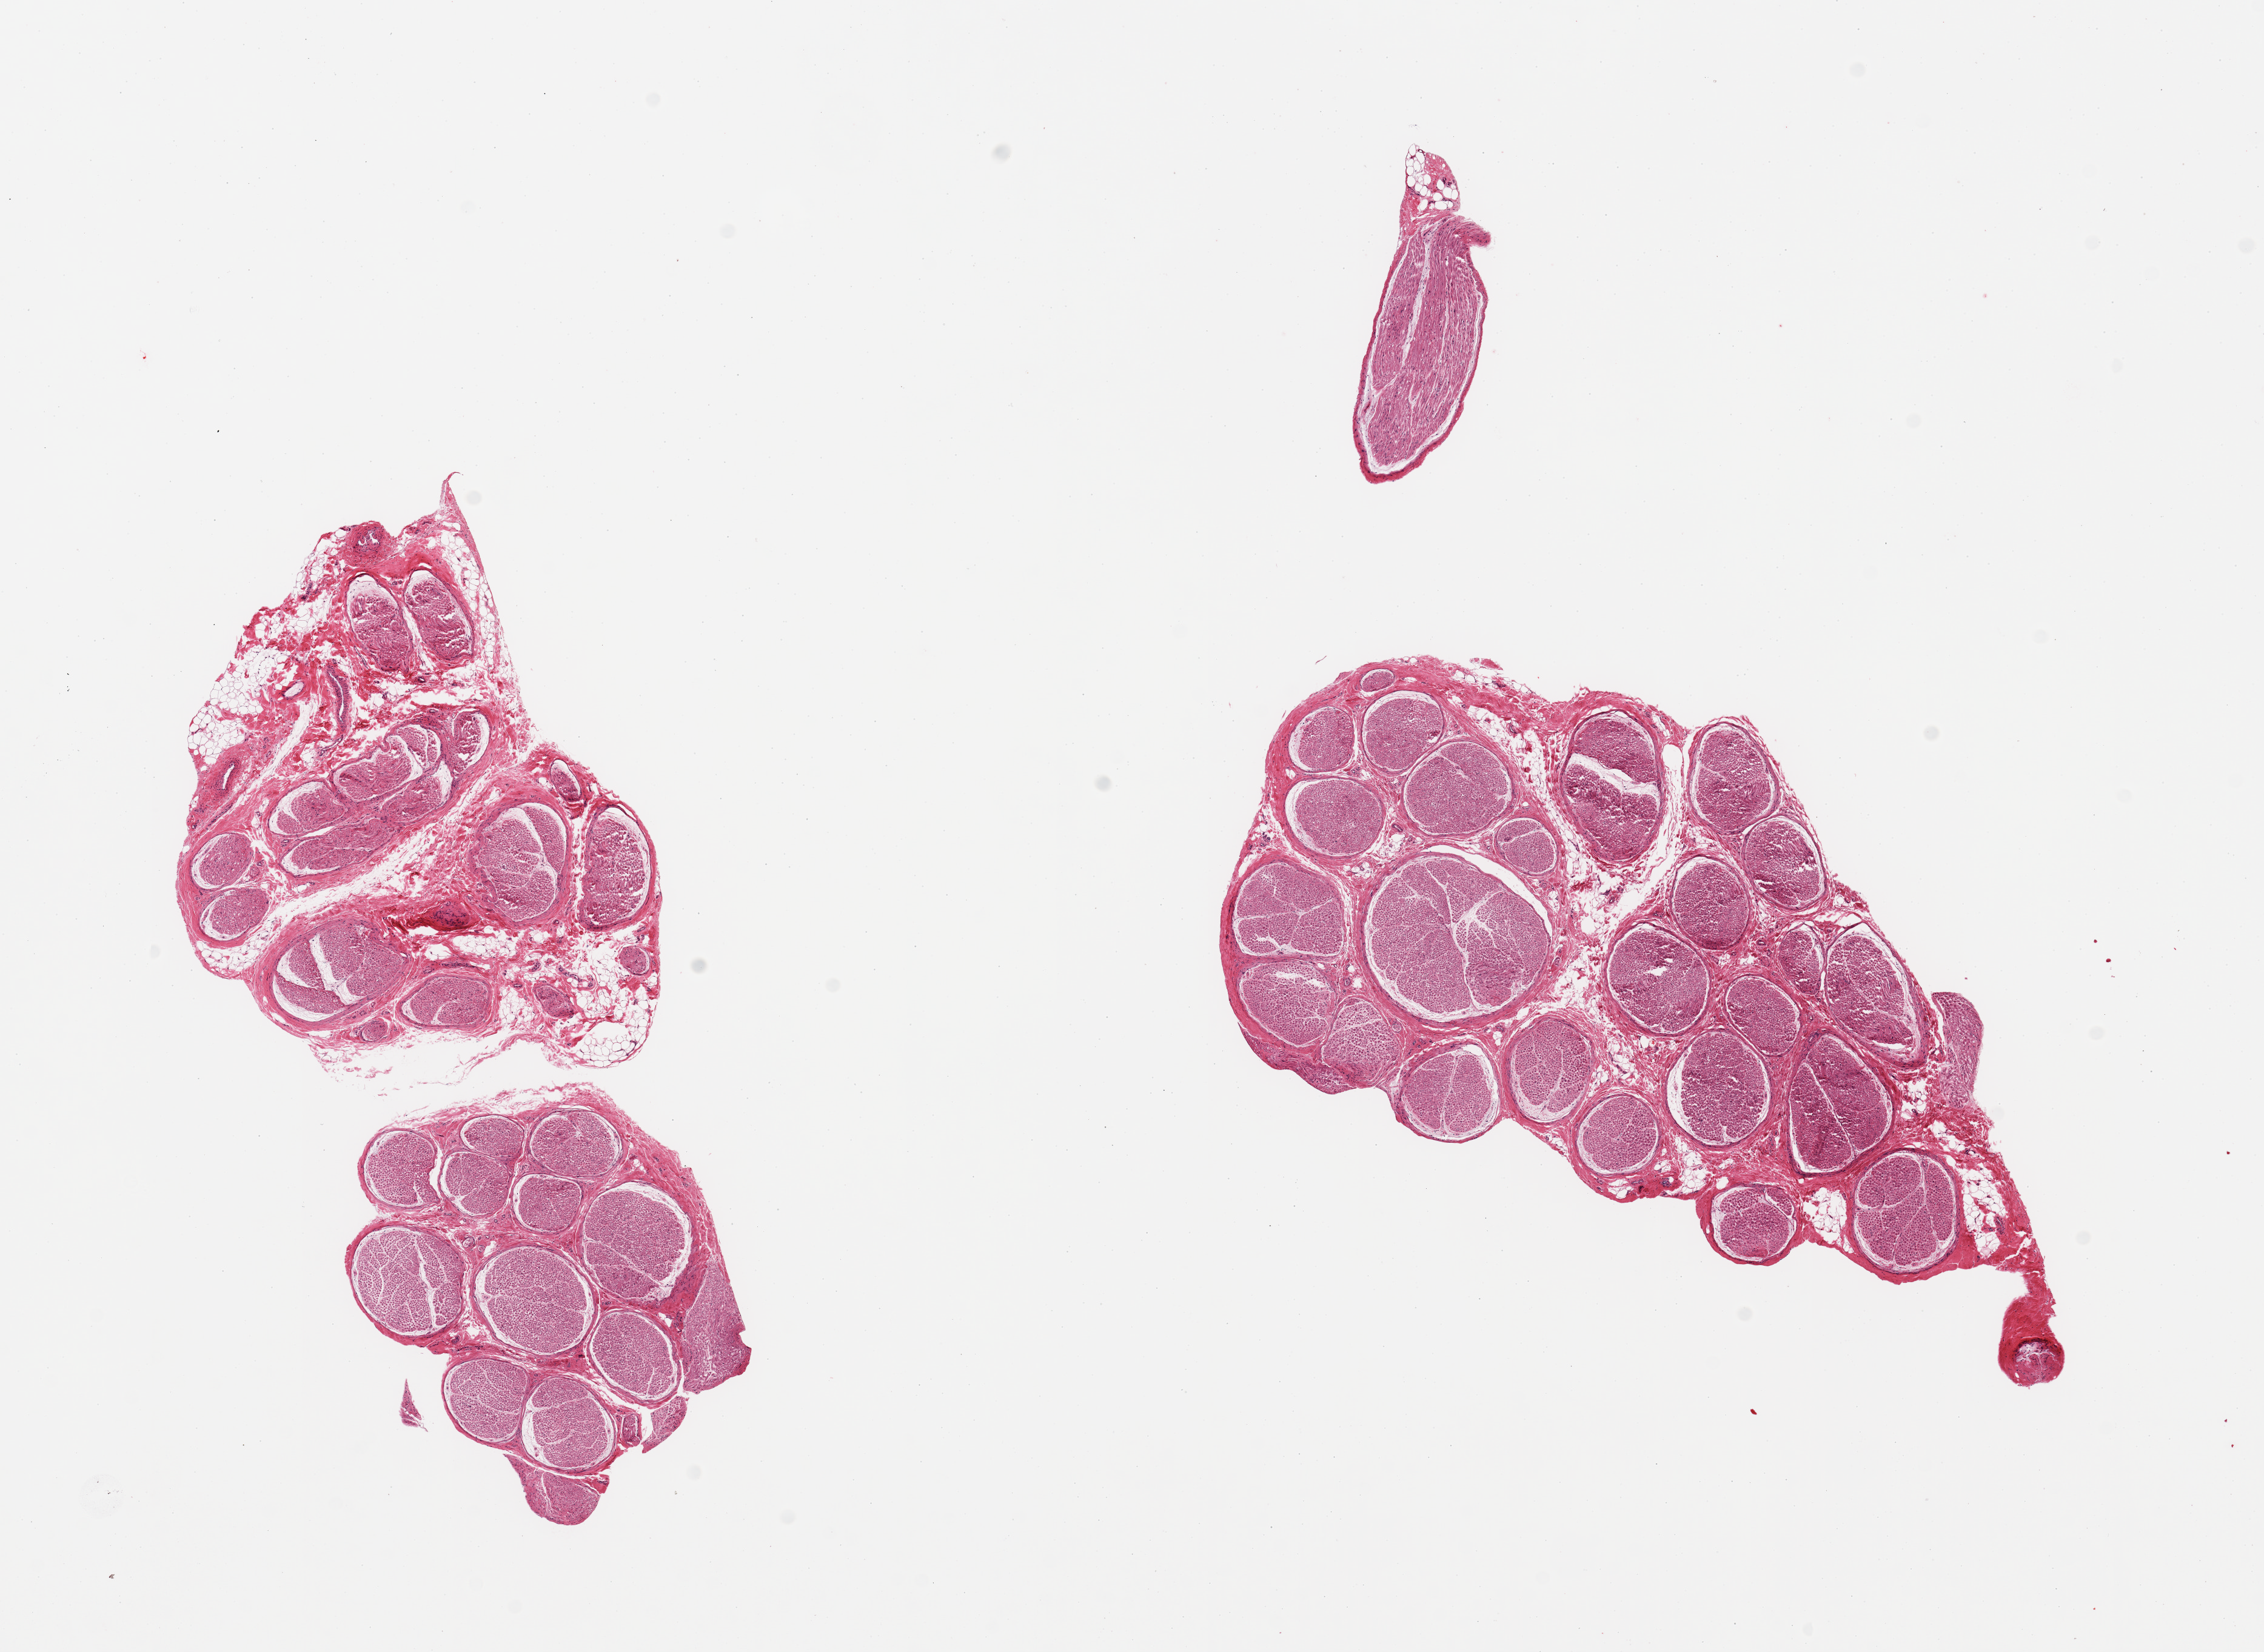
Haematoxylin and eosin whole-slide image, brightfield, low-resolution overview of the scanned area, about 14.8 x 10.8 mm. PAXgene-fixed paraffin-embedded (PFPE) section. Target tissue: tibial nerve. Donor tissue sample. Donor: female.
Review note (as recorded): 4 pieces; ~5-10% internal and external fat.